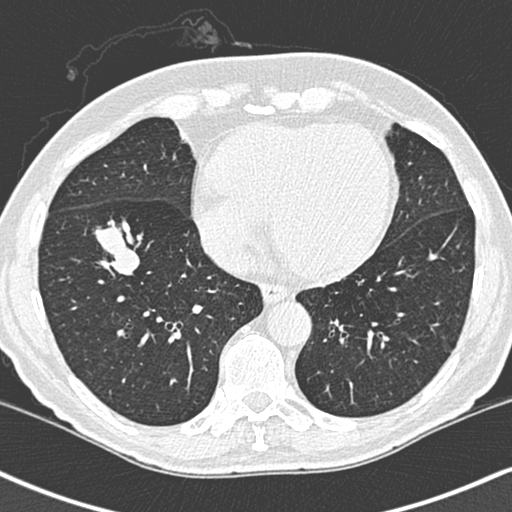
Low-dose screening chest CT, one axial slice; slice 94 of 248 in the series (ordered by position); 120 kVp; lung window (W 1500 / L -600 HU); 512 × 512 image matrix.
Annotated regions visible in this slice (expert manual segmentation):
- lesion 1 (tumor, lower lobe of right lung): bounding box [x1, y1, x2, y2] px = [94, 181, 140, 238]